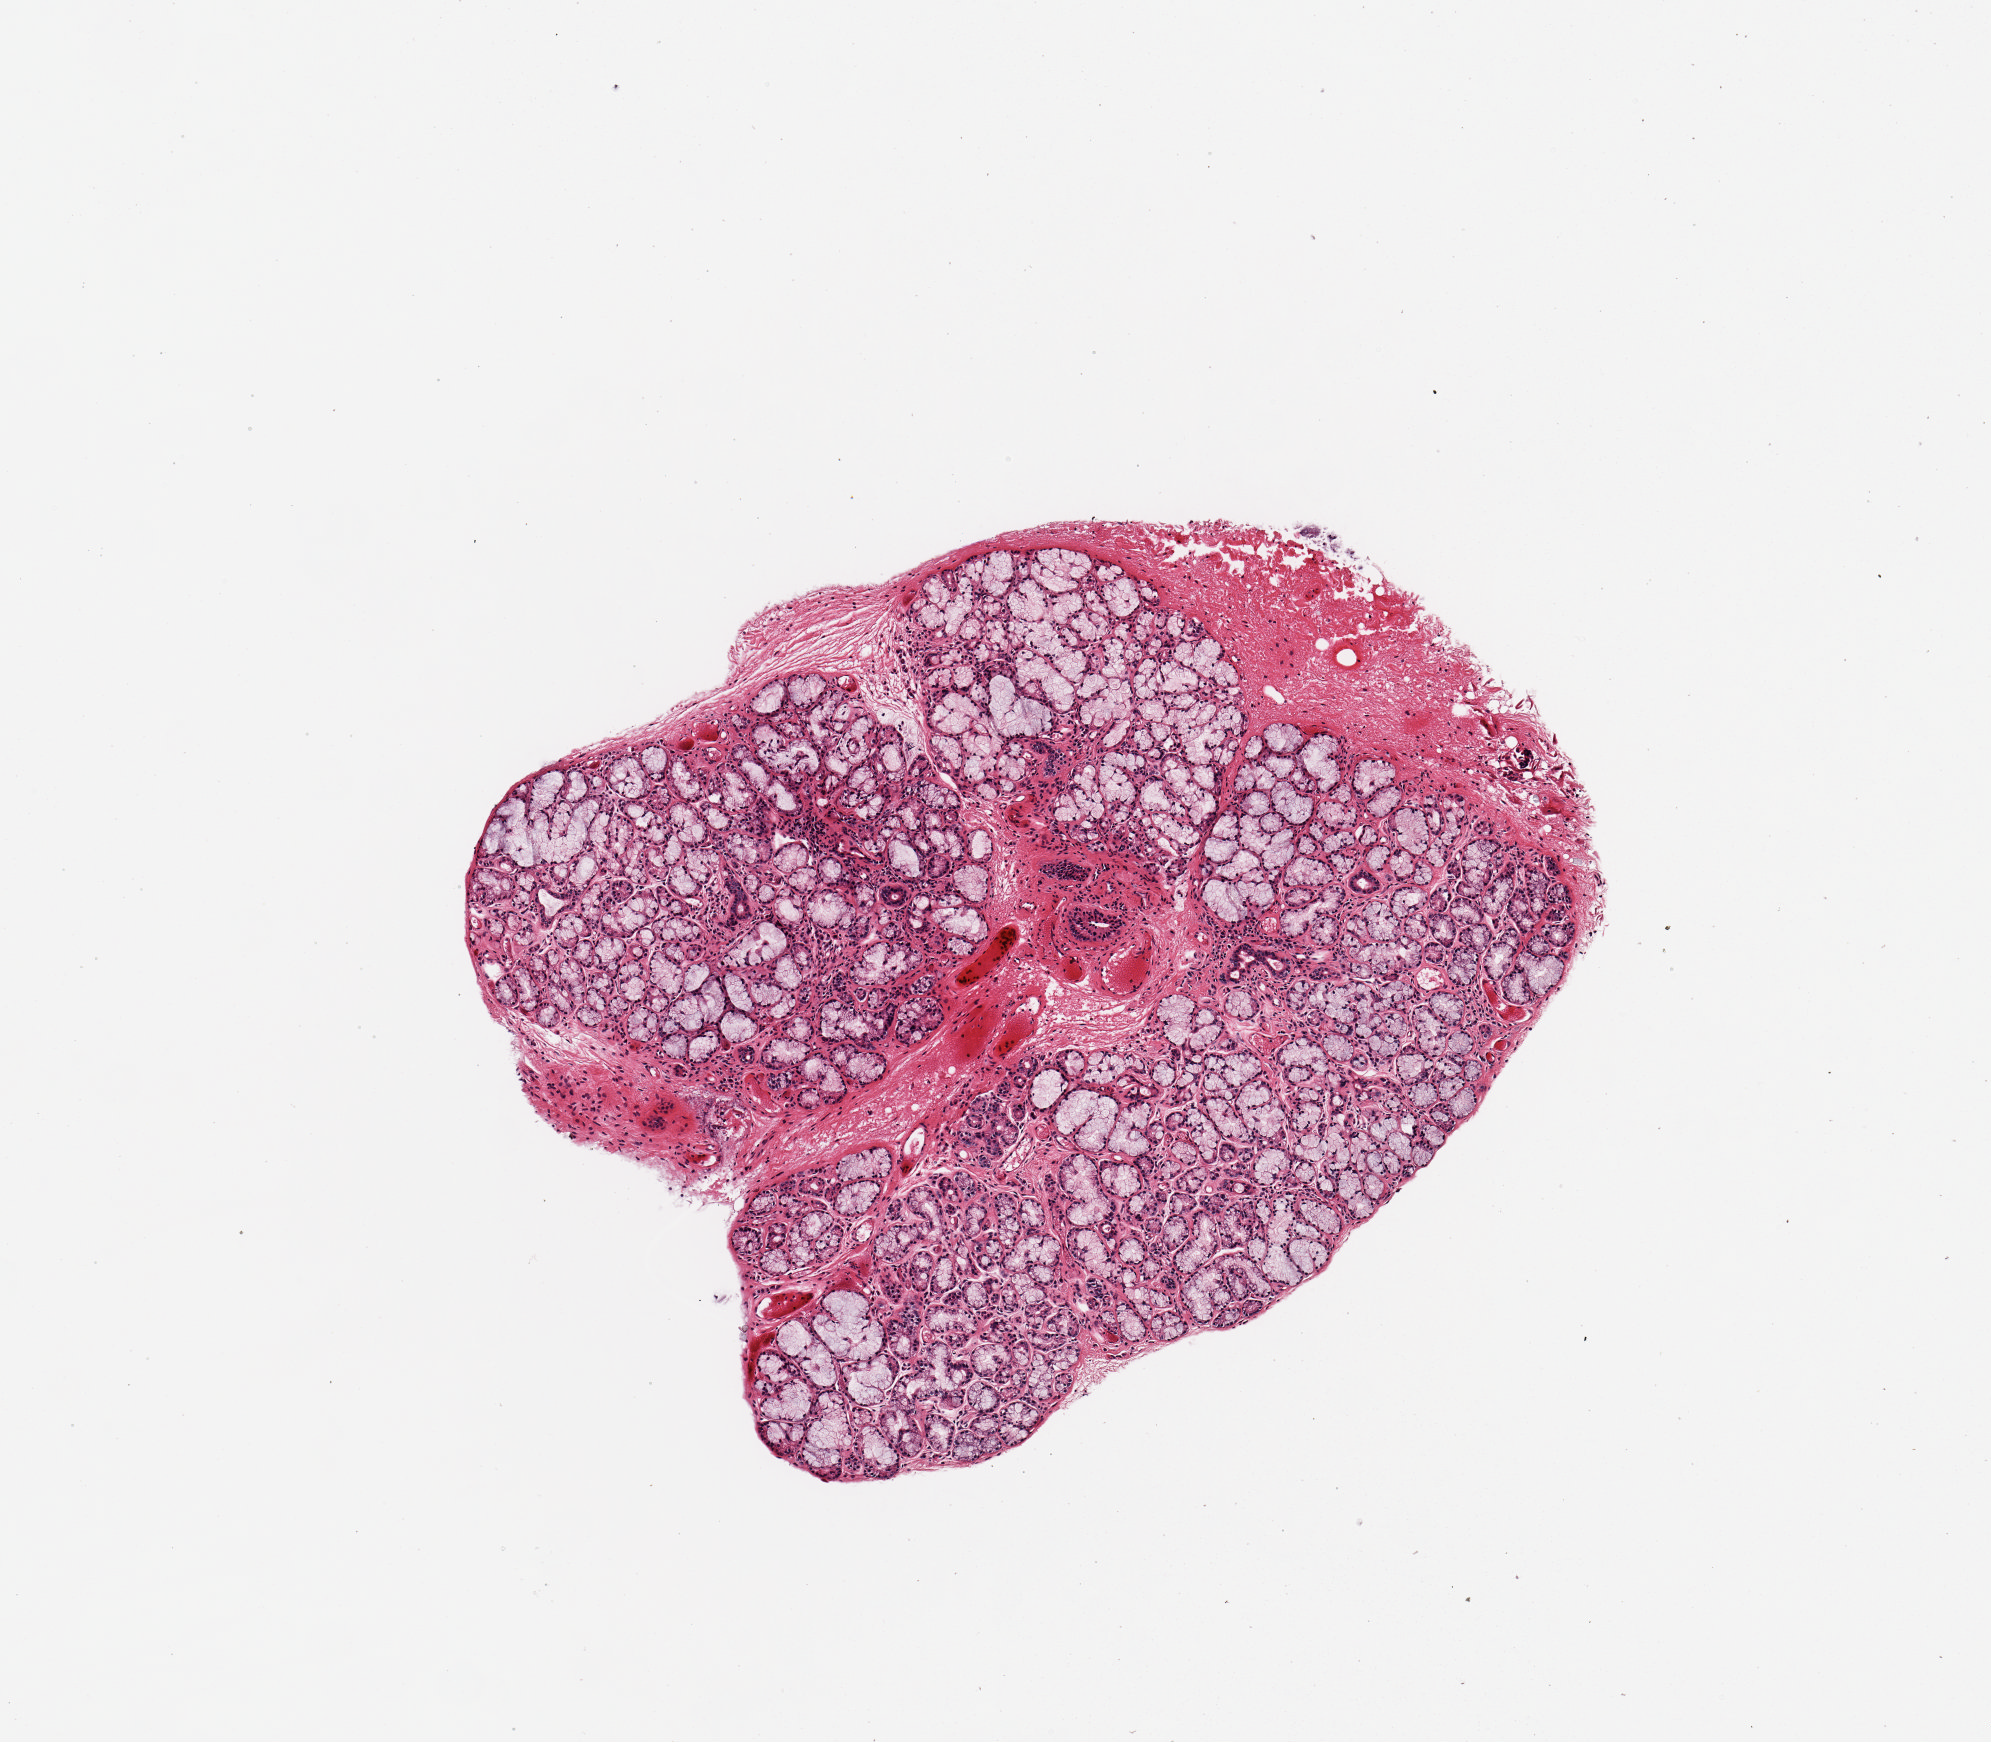
Whole-slide image, hematoxylin and eosin (H&E) stain — whole scanned area (about 3.9 x 3.4 mm, acquisition: 20x scan) shown as a low-resolution overview. PAXgene-fixed paraffin-embedded (PFPE) section. Sampled site (target tissue): minor salivary gland. Tissue donor sample.
Review note (as recorded): 1 piece; well dissected gland with only small fibrous content.